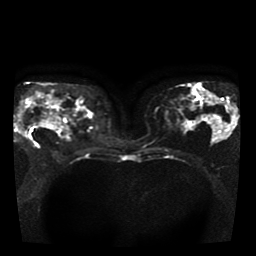
Breast MRI, one axial slice. Position 21 of 41 along the scan axis. Diffusion-weighted series; image 2 of 4 stored at this slice position (different b-values; order by instance number). 1.5 T. 5 mm slice thickness. 256 × 256 image matrix, field of view 330 × 330 mm. Female patient.
Structures marked on this image (outlined manually by an expert reader):
- tumour on diffusion-weighted imaging: bounding box <18,103,36,134> (left, top, right, bottom; pixels)